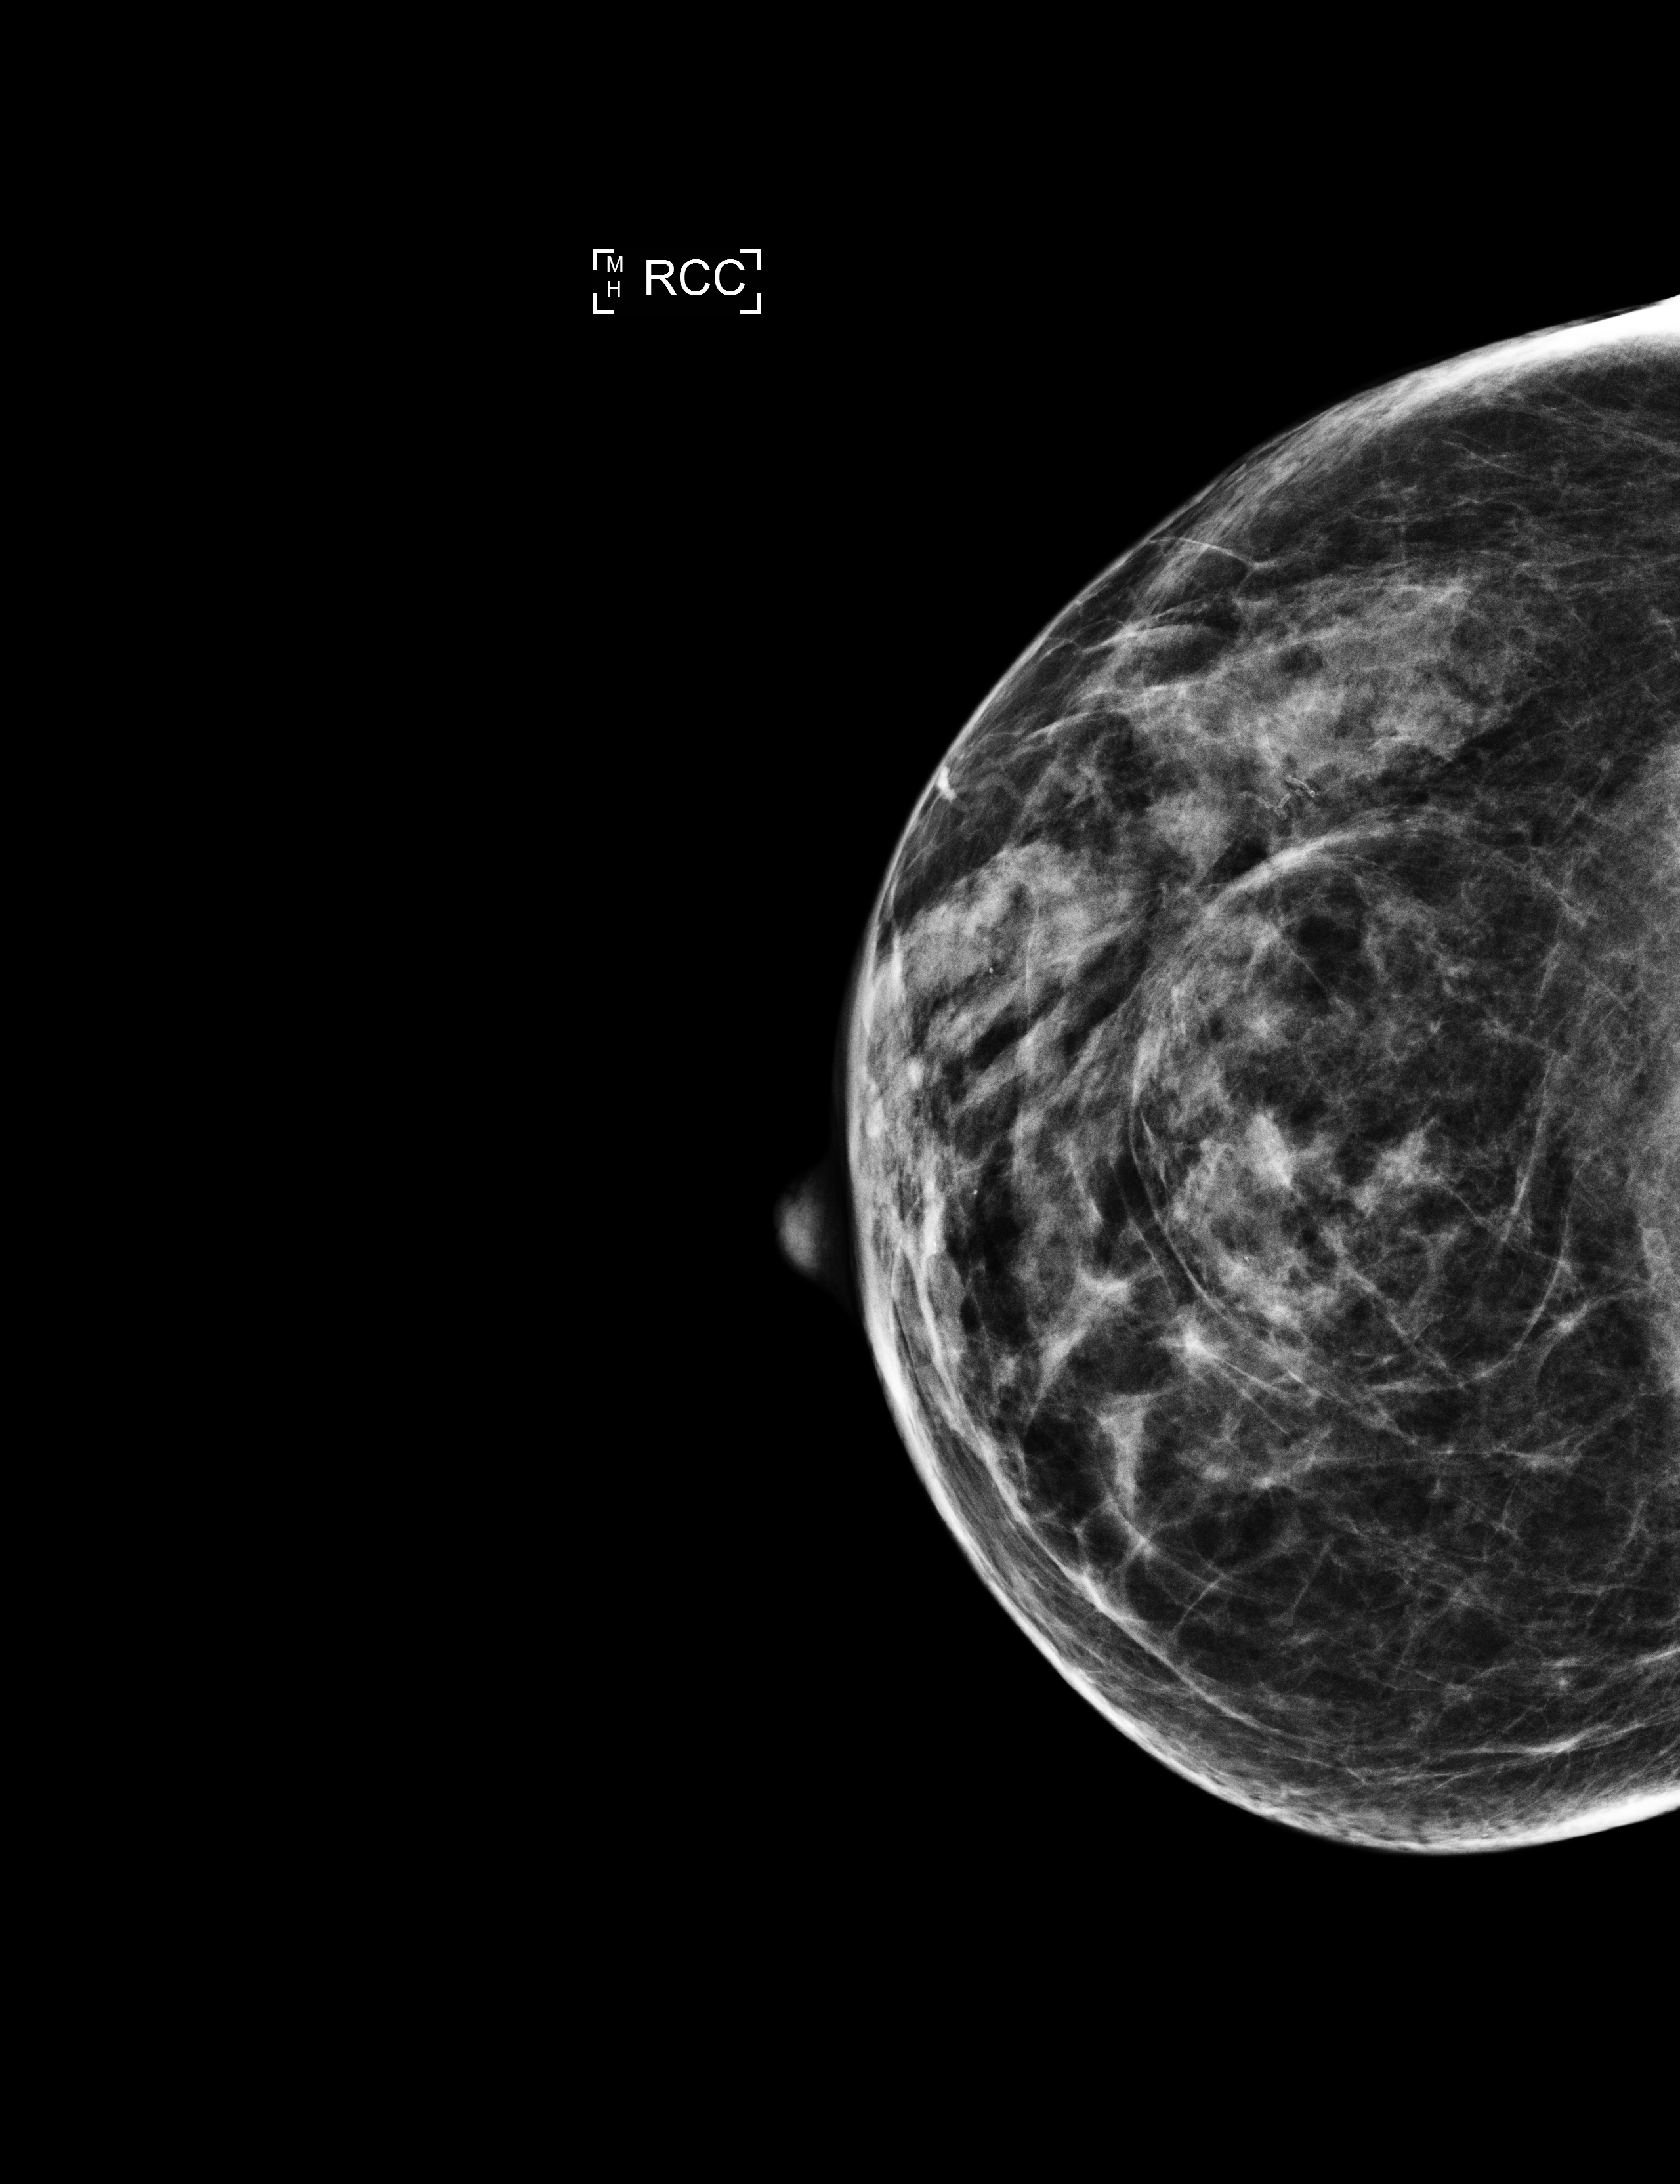
Annual screening mammography examination, system: Selenia Dimensions.
Image type: full-field digital mammogram. Breast: right. Projection: CC view.